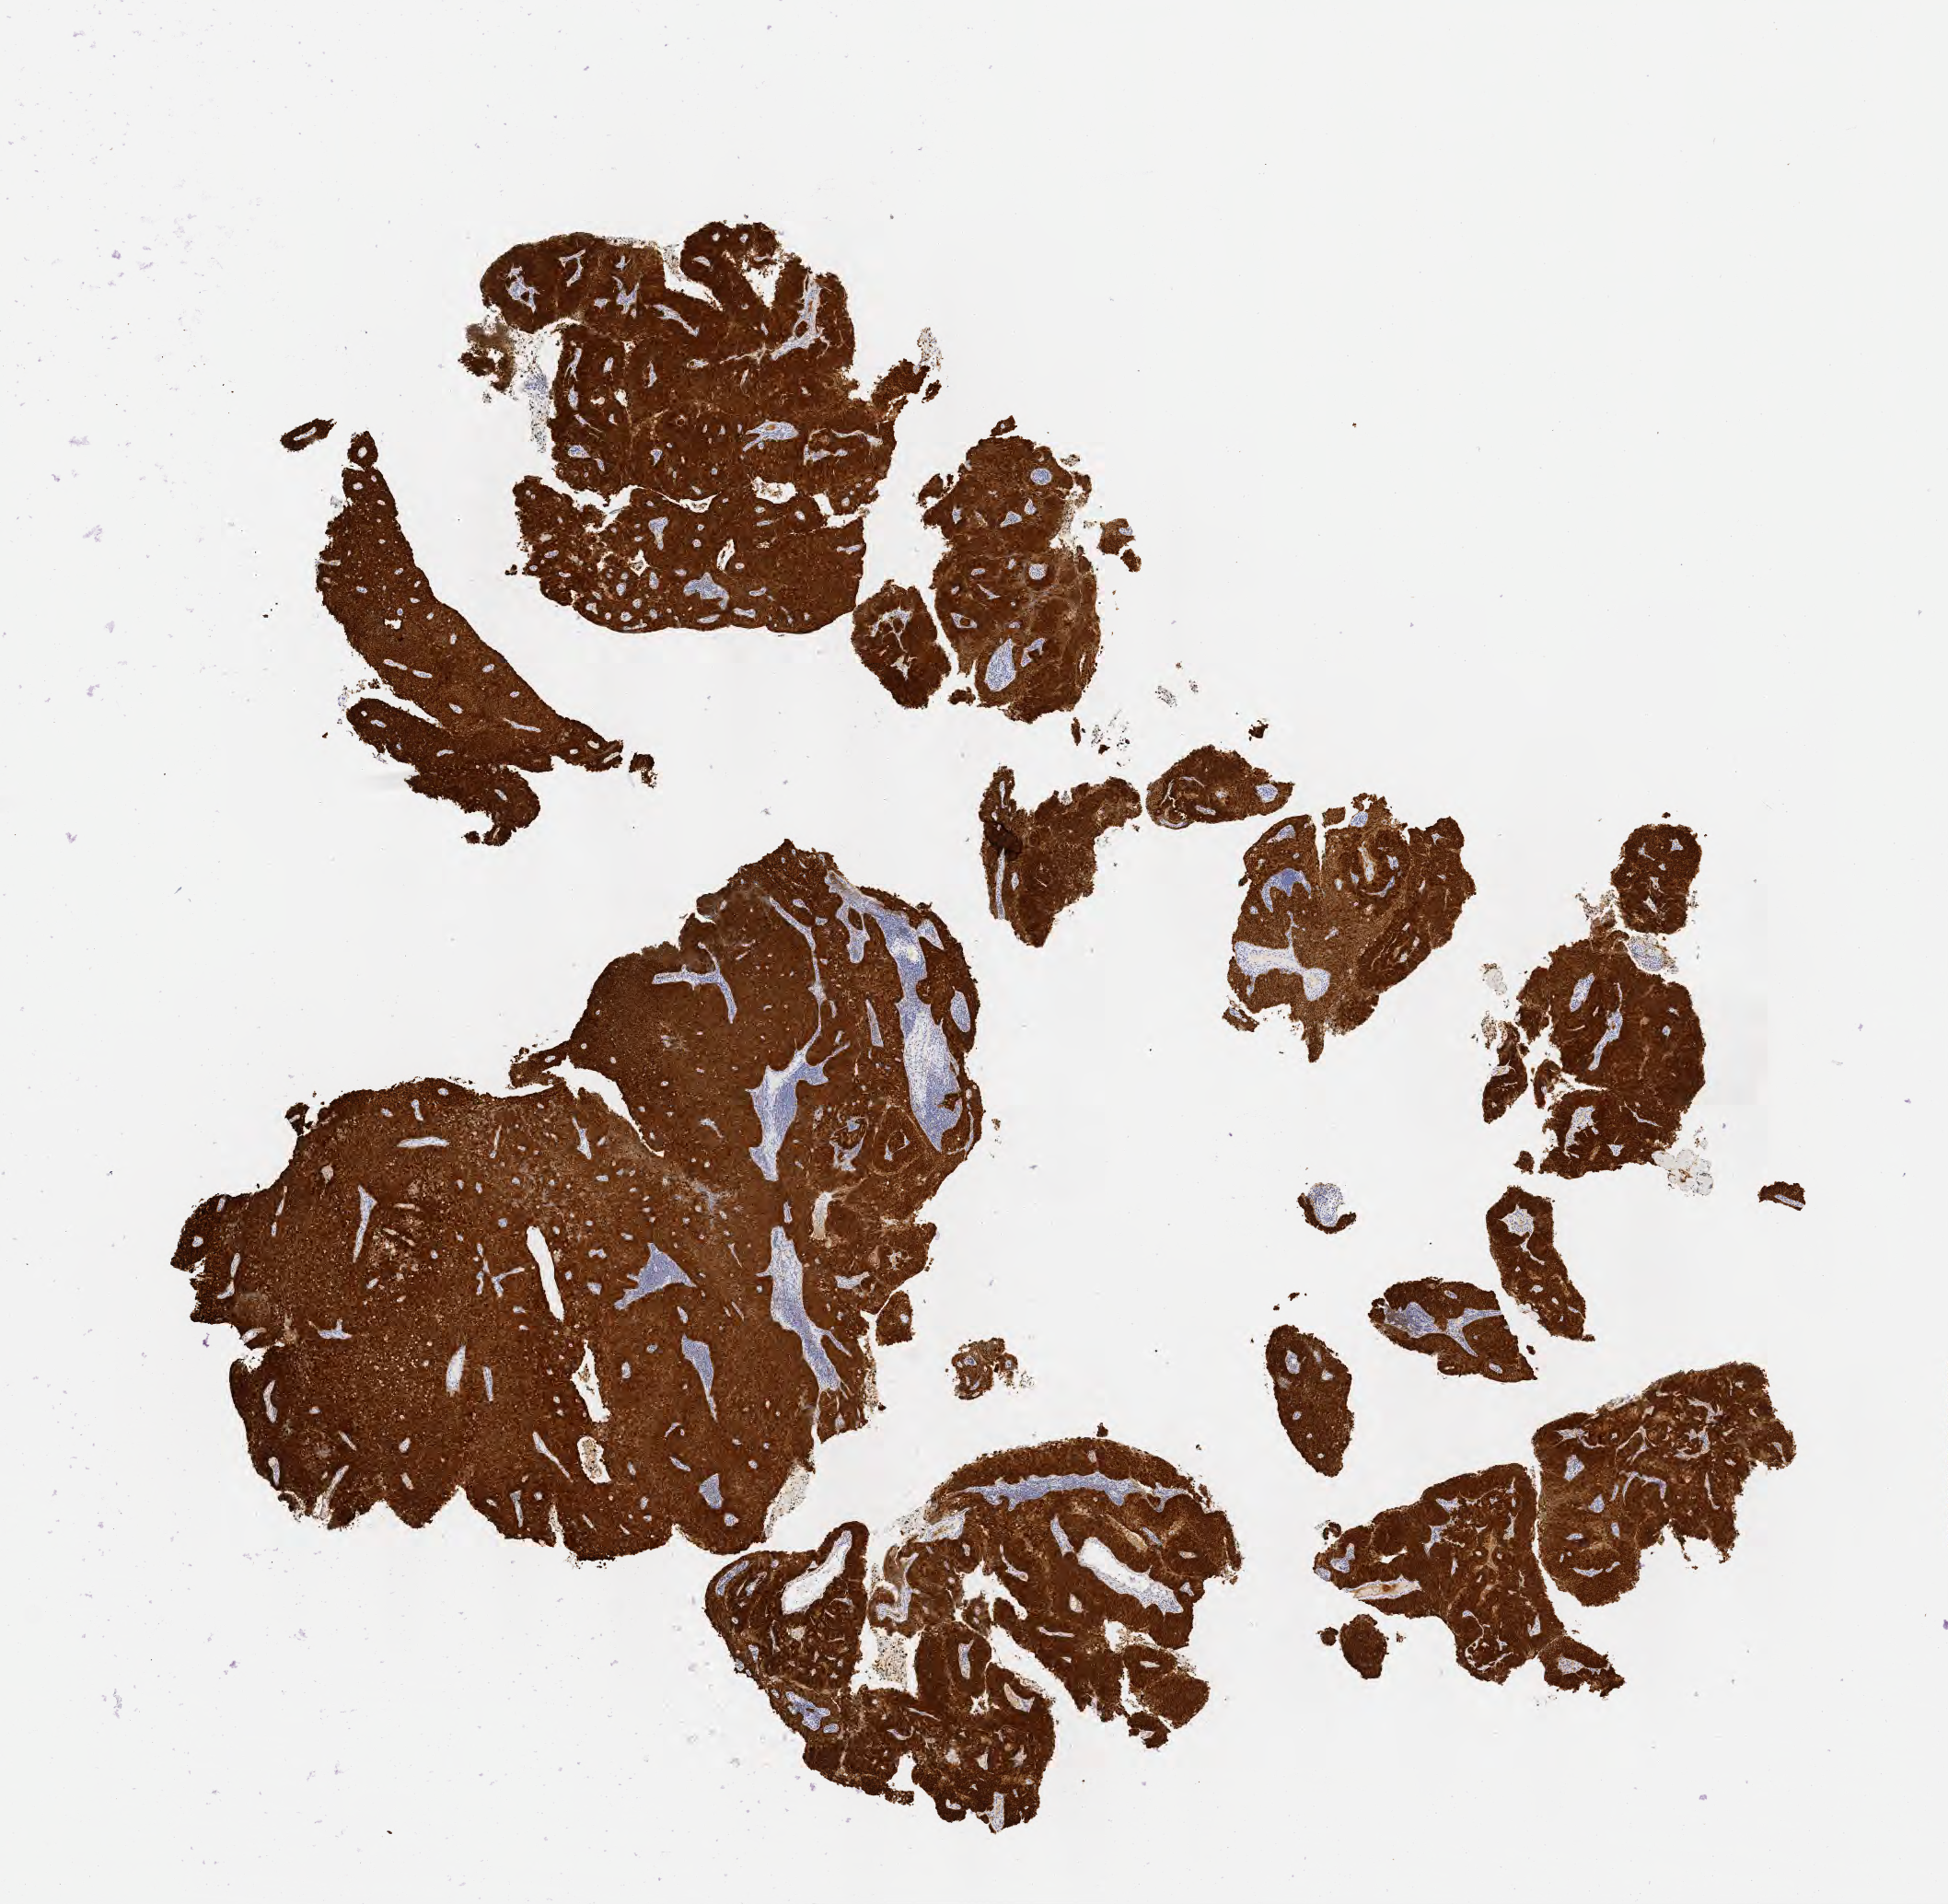
IHC for p16 (p16INK4a), whole-slide image — low-resolution overview of the scanned area, about 8.6 x 8.4 mm. Specimen: tumor tissue. Site: cervix. Female patient, aged 47.
Histologic diagnosis: Squamous cell carcinoma, keratinizing, NOS.